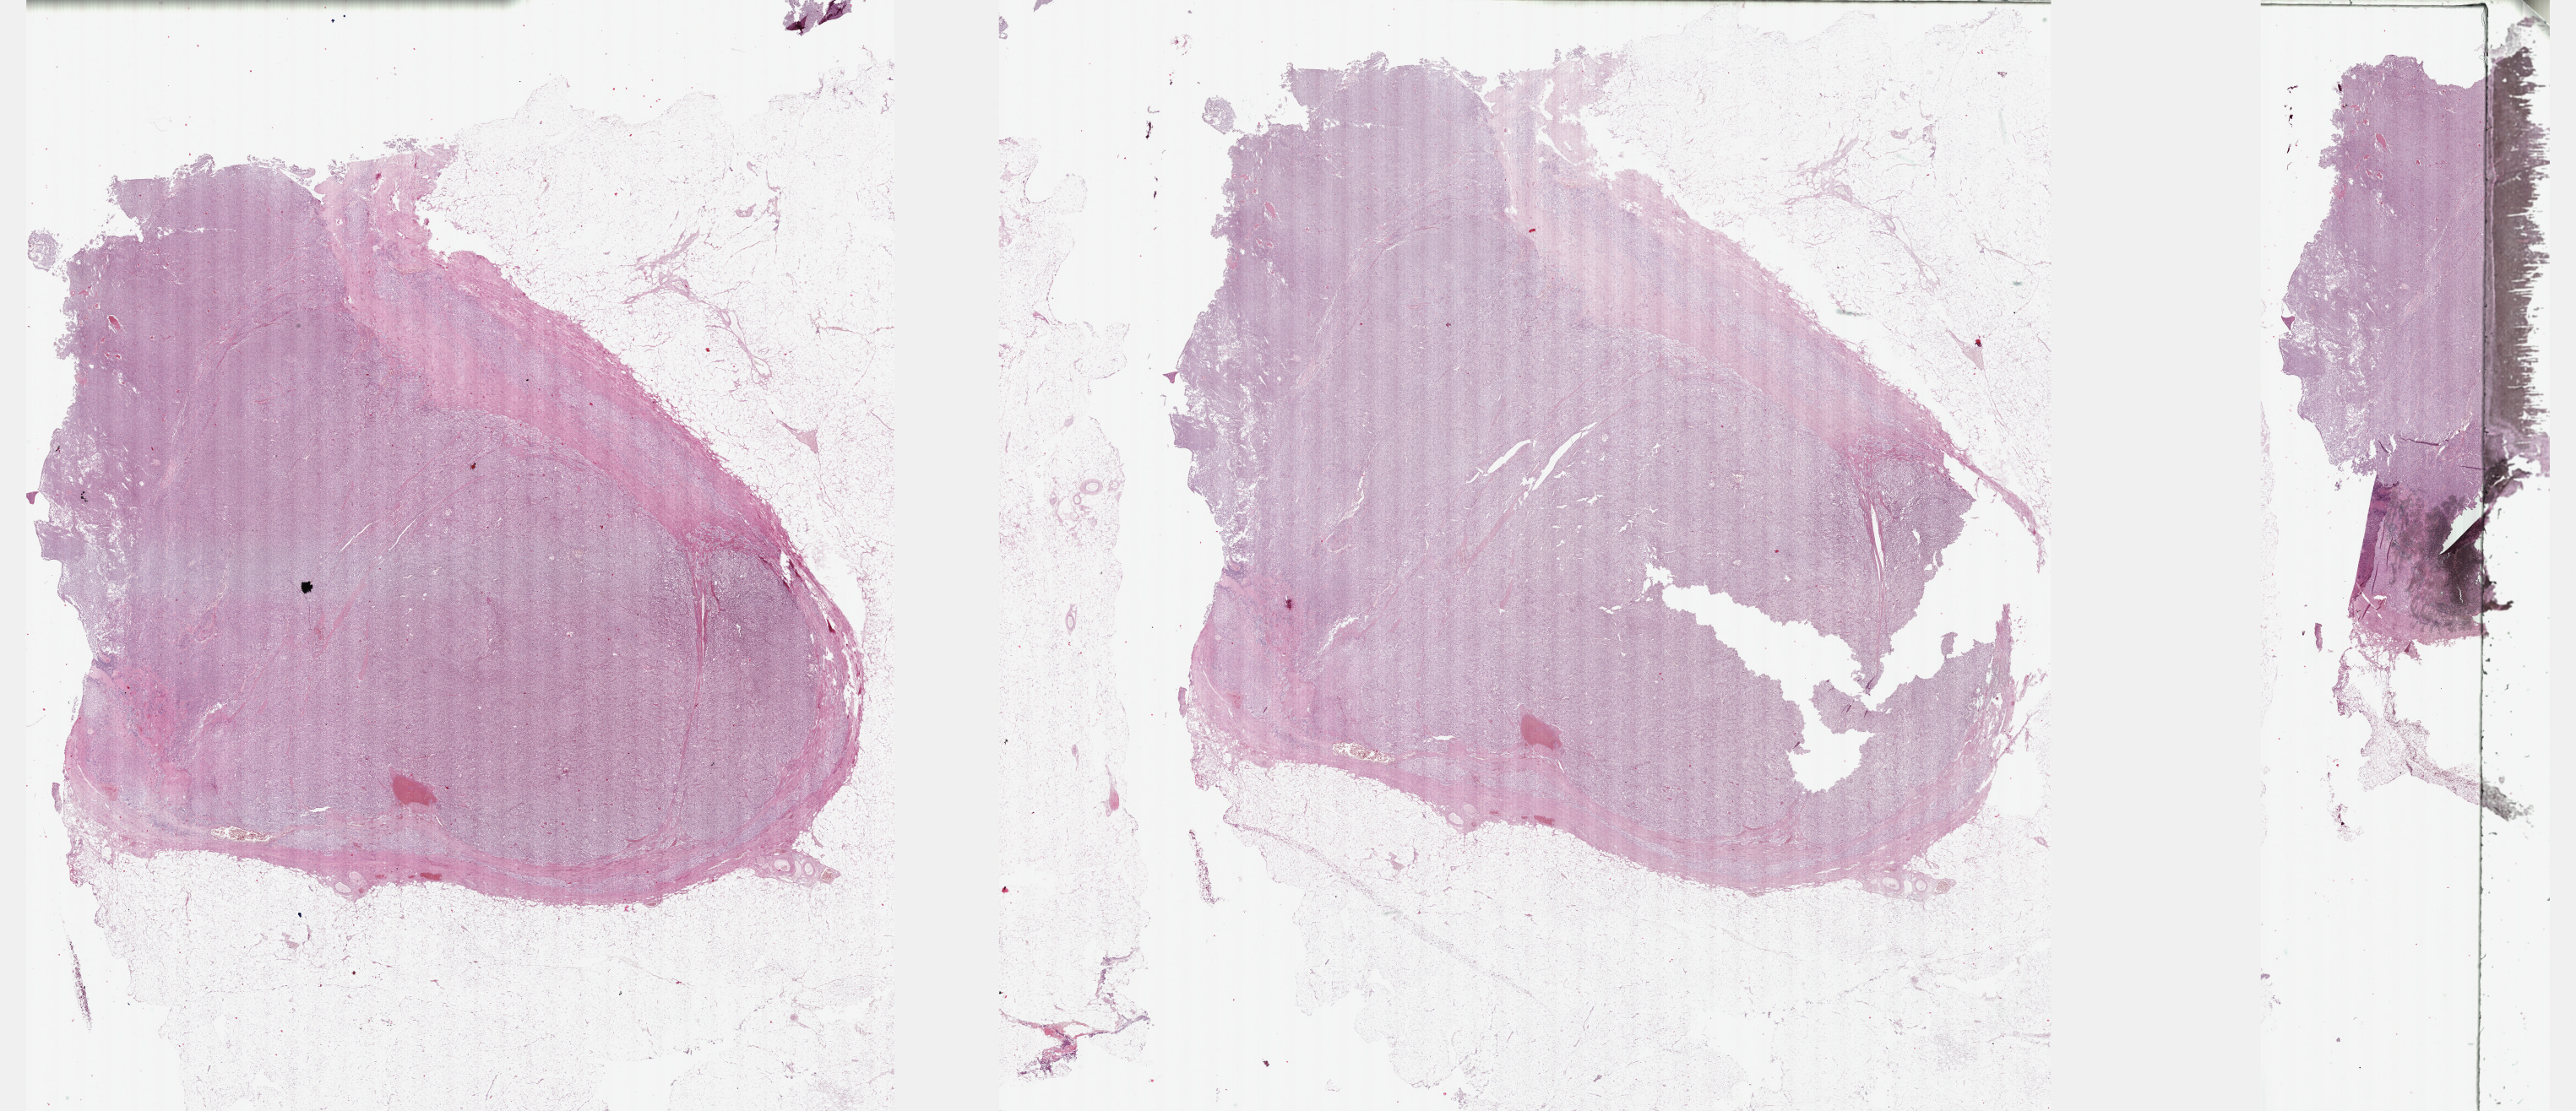
Digitized H&E tissue section (whole slide), whole scanned area (about 49.3 x 21.3 mm, acquisition: 40x scan) shown as a low-resolution overview, FFPE section, adrenal gland, primary tumour sample. Patient: female, age at initial diagnosis 59 years.
Lymph nodes positive (case pathology): 0 of 1 examined. Histologic diagnosis: Pheochromocytoma, NOS.